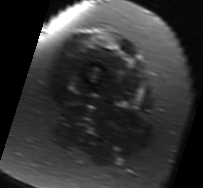
MRI of an extremity soft-tissue mass, one axial slice. Slice 10 of 91 in the series (ordered by position). T2-weighted fat-saturated. MR volume resampled by the dataset authors to the PET/CT grid (not the native acquisition matrix). 203 × 188 image matrix. Female patient. Case-level facts recorded for this patient, not image findings: histological type: malignant solitary fibrous tumor; grade: intermediate; site of the primary tumour: right thigh.
Outlined on this slice (expert contour drawn on MRI and transferred to this co-registered scan by the dataset authors):
- gross tumour volume including surrounding oedema: box from (x=92, y=40) to (x=132, y=64) px